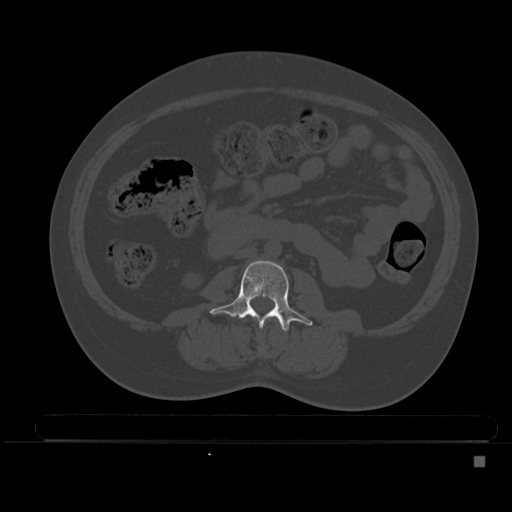
CT including the spine, one axial slice. Slice 154 of 495 in the series (ordered by position). Bone window (W 1800 / L 400 HU). 512 × 512 image matrix. Female patient, age 33 years. Case-level facts recorded for this patient, not image findings: primary cancer: breast; vertebrae with lytic lesions (as recorded): T1.
Structures marked on this image (semi-automatic segmentation, software-assisted and operator-edited):
- L2 vertebra: box from (x=275, y=318) to (x=282, y=329) px
- L3 vertebra: (x=210, y=261)–(x=313, y=332)